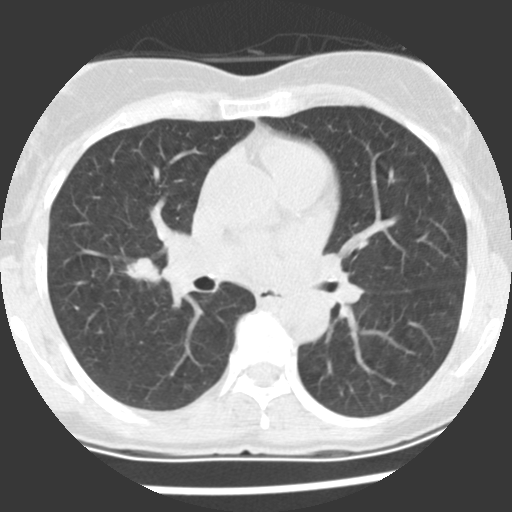
Low-dose screening chest CT, axial slice; first (baseline) screen; lung window (W 1500 / L -600 HU); 2.5 mm slice thickness; 512 × 512 image matrix, field of view 270 × 270 mm. Female participant, aged 60 years at enrolment.
Expert reader's lesion annotation, bounding box [x1, y1, x2, y2] px = [115, 252, 173, 297]. The screening reader recorded 2 non-calcified nodules or masses ≥4 mm on this exam; which of them this box marks is not recorded. Official screen result: positive, change unspecified: nodule(s) >= 4 mm or enlarging nodule(s), mass(es), or other non-specific abnormalities suspicious for lung cancer. Later outcome: lung cancer diagnosed 10 days after this screen — adenocarcinoma, NOS, right upper lobe, stage IIIA (AJCC 6th edition), 20 mm at pathology.